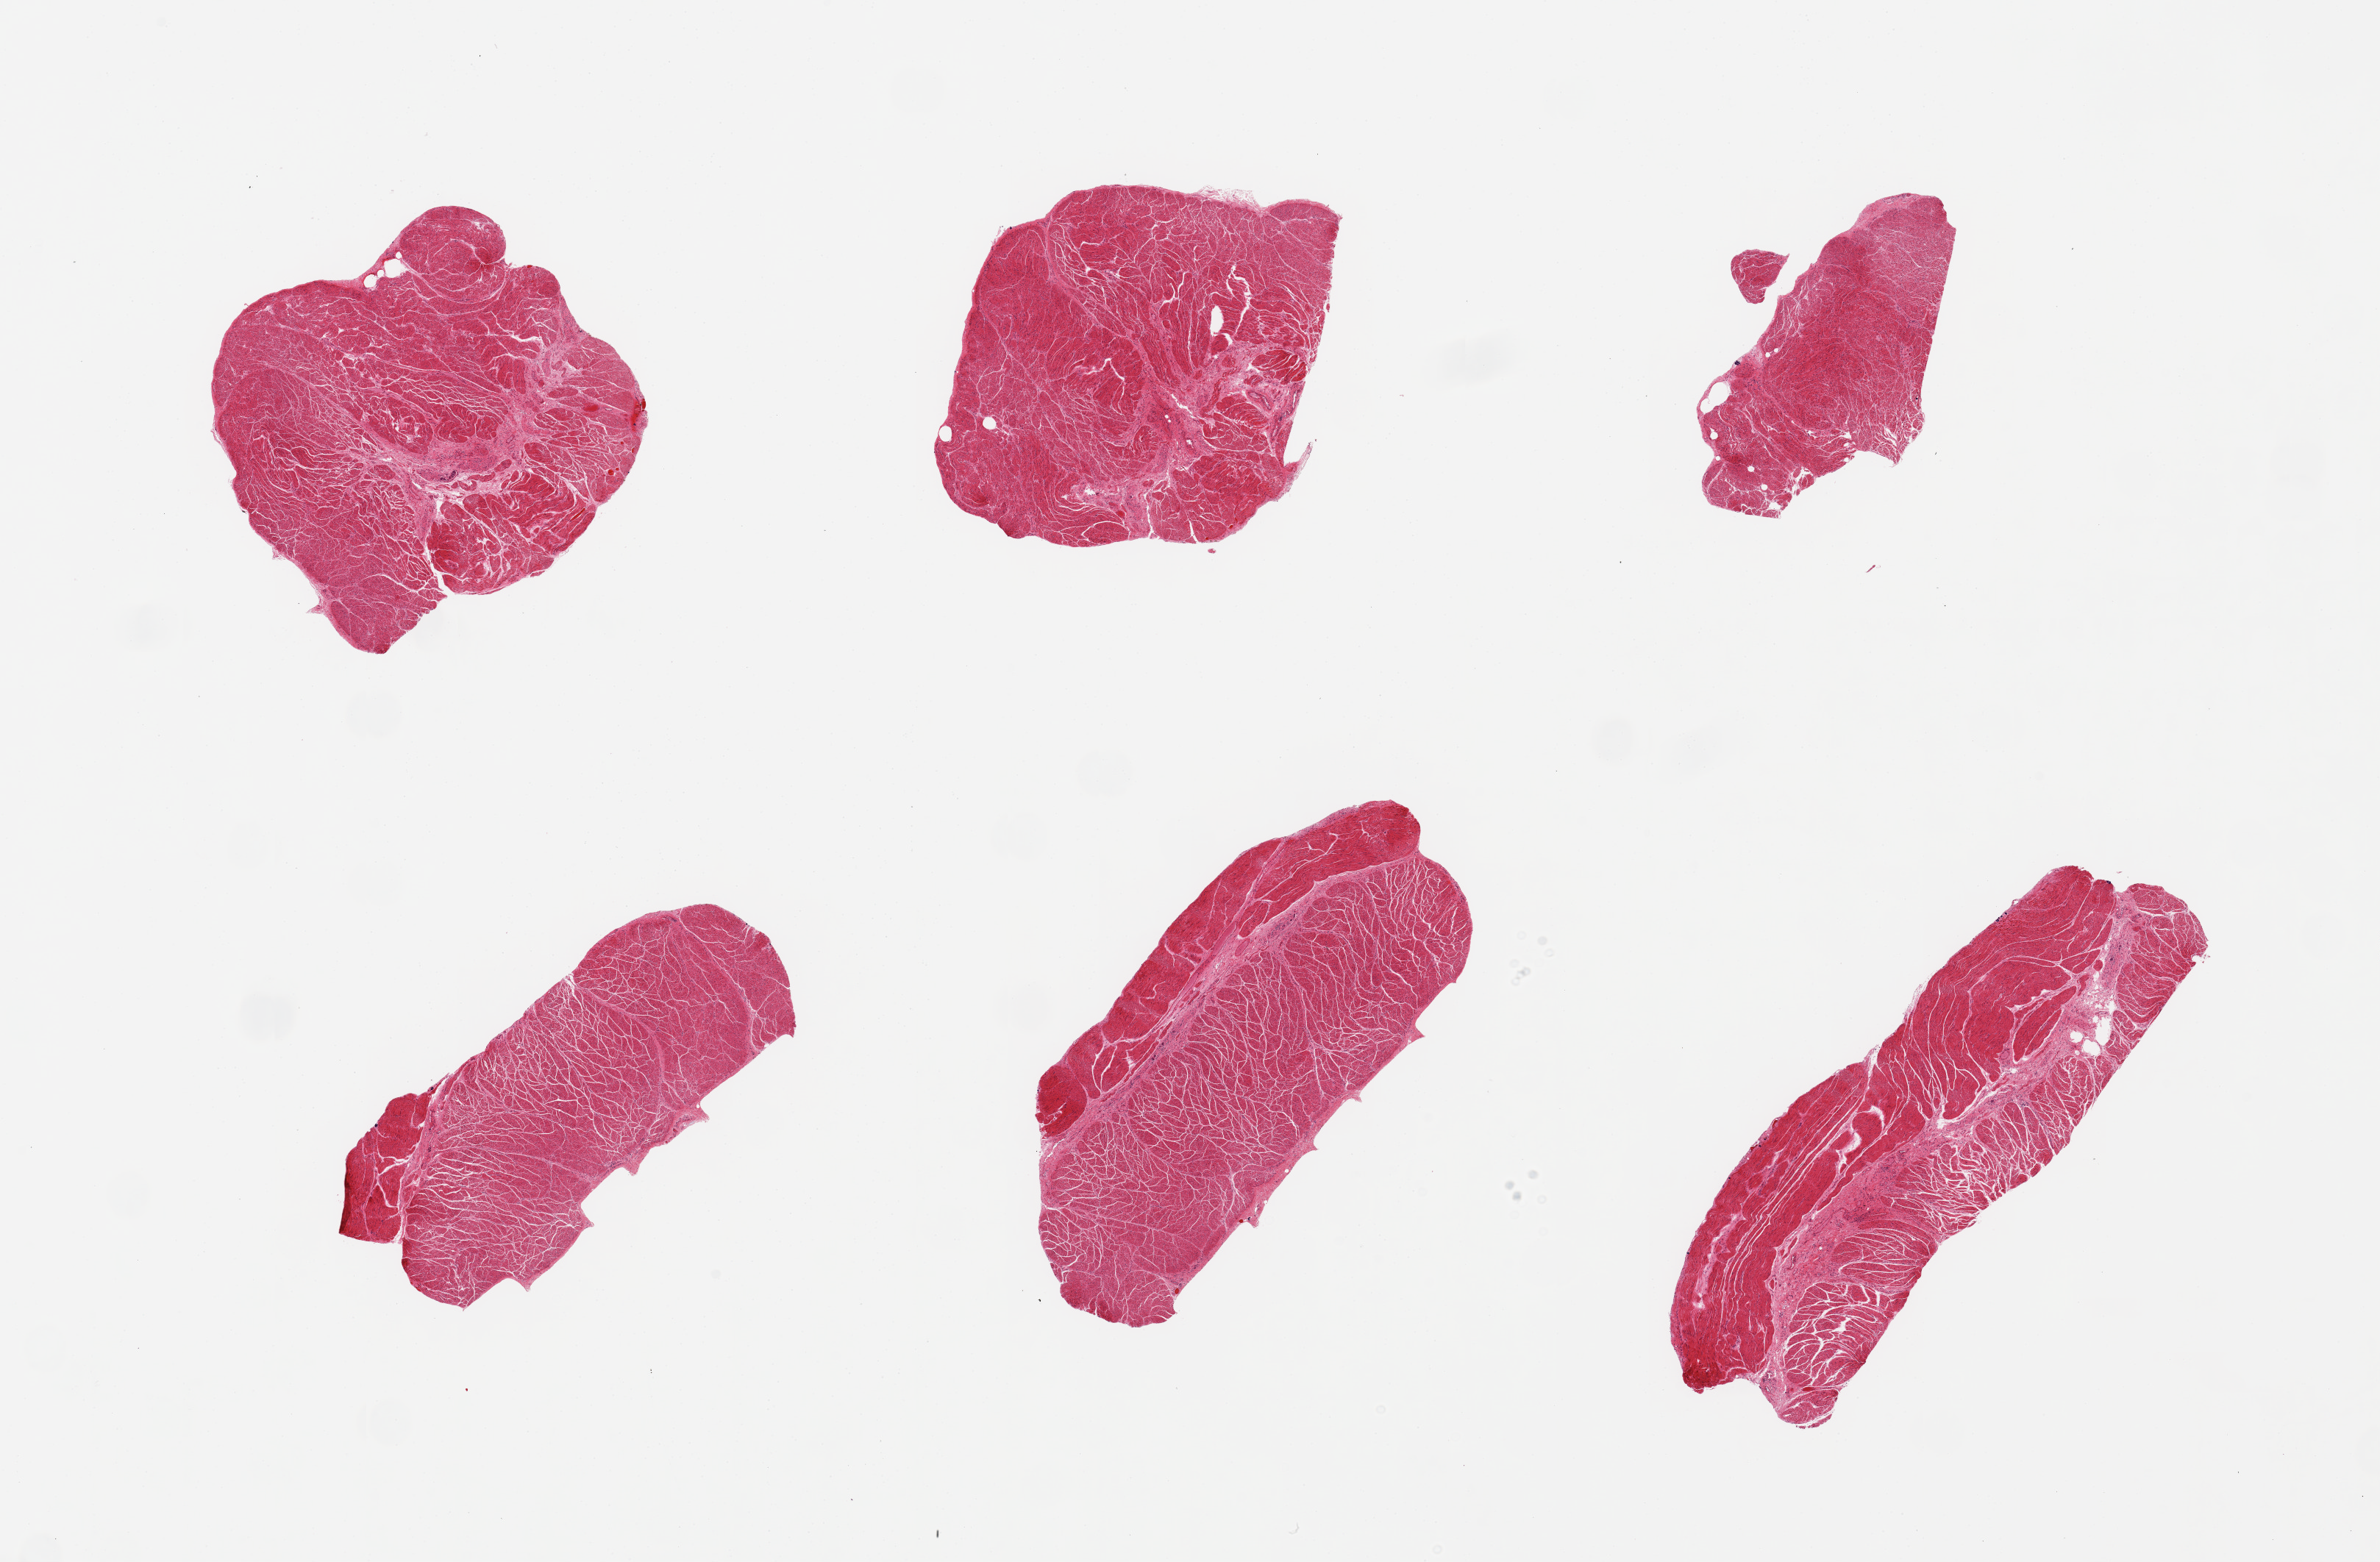
Digitized H&E-stained section, brightfield — shown as a low-resolution overview of the whole scanned area (about 25.6 x 16.8 mm). PAXgene-fixed paraffin-embedded (PFPE) section. Section of esophageal muscle (target tissue). Donor tissue sample. Male donor.
- reviewer comment on this tissue sample: 6 pieces; well trimmed